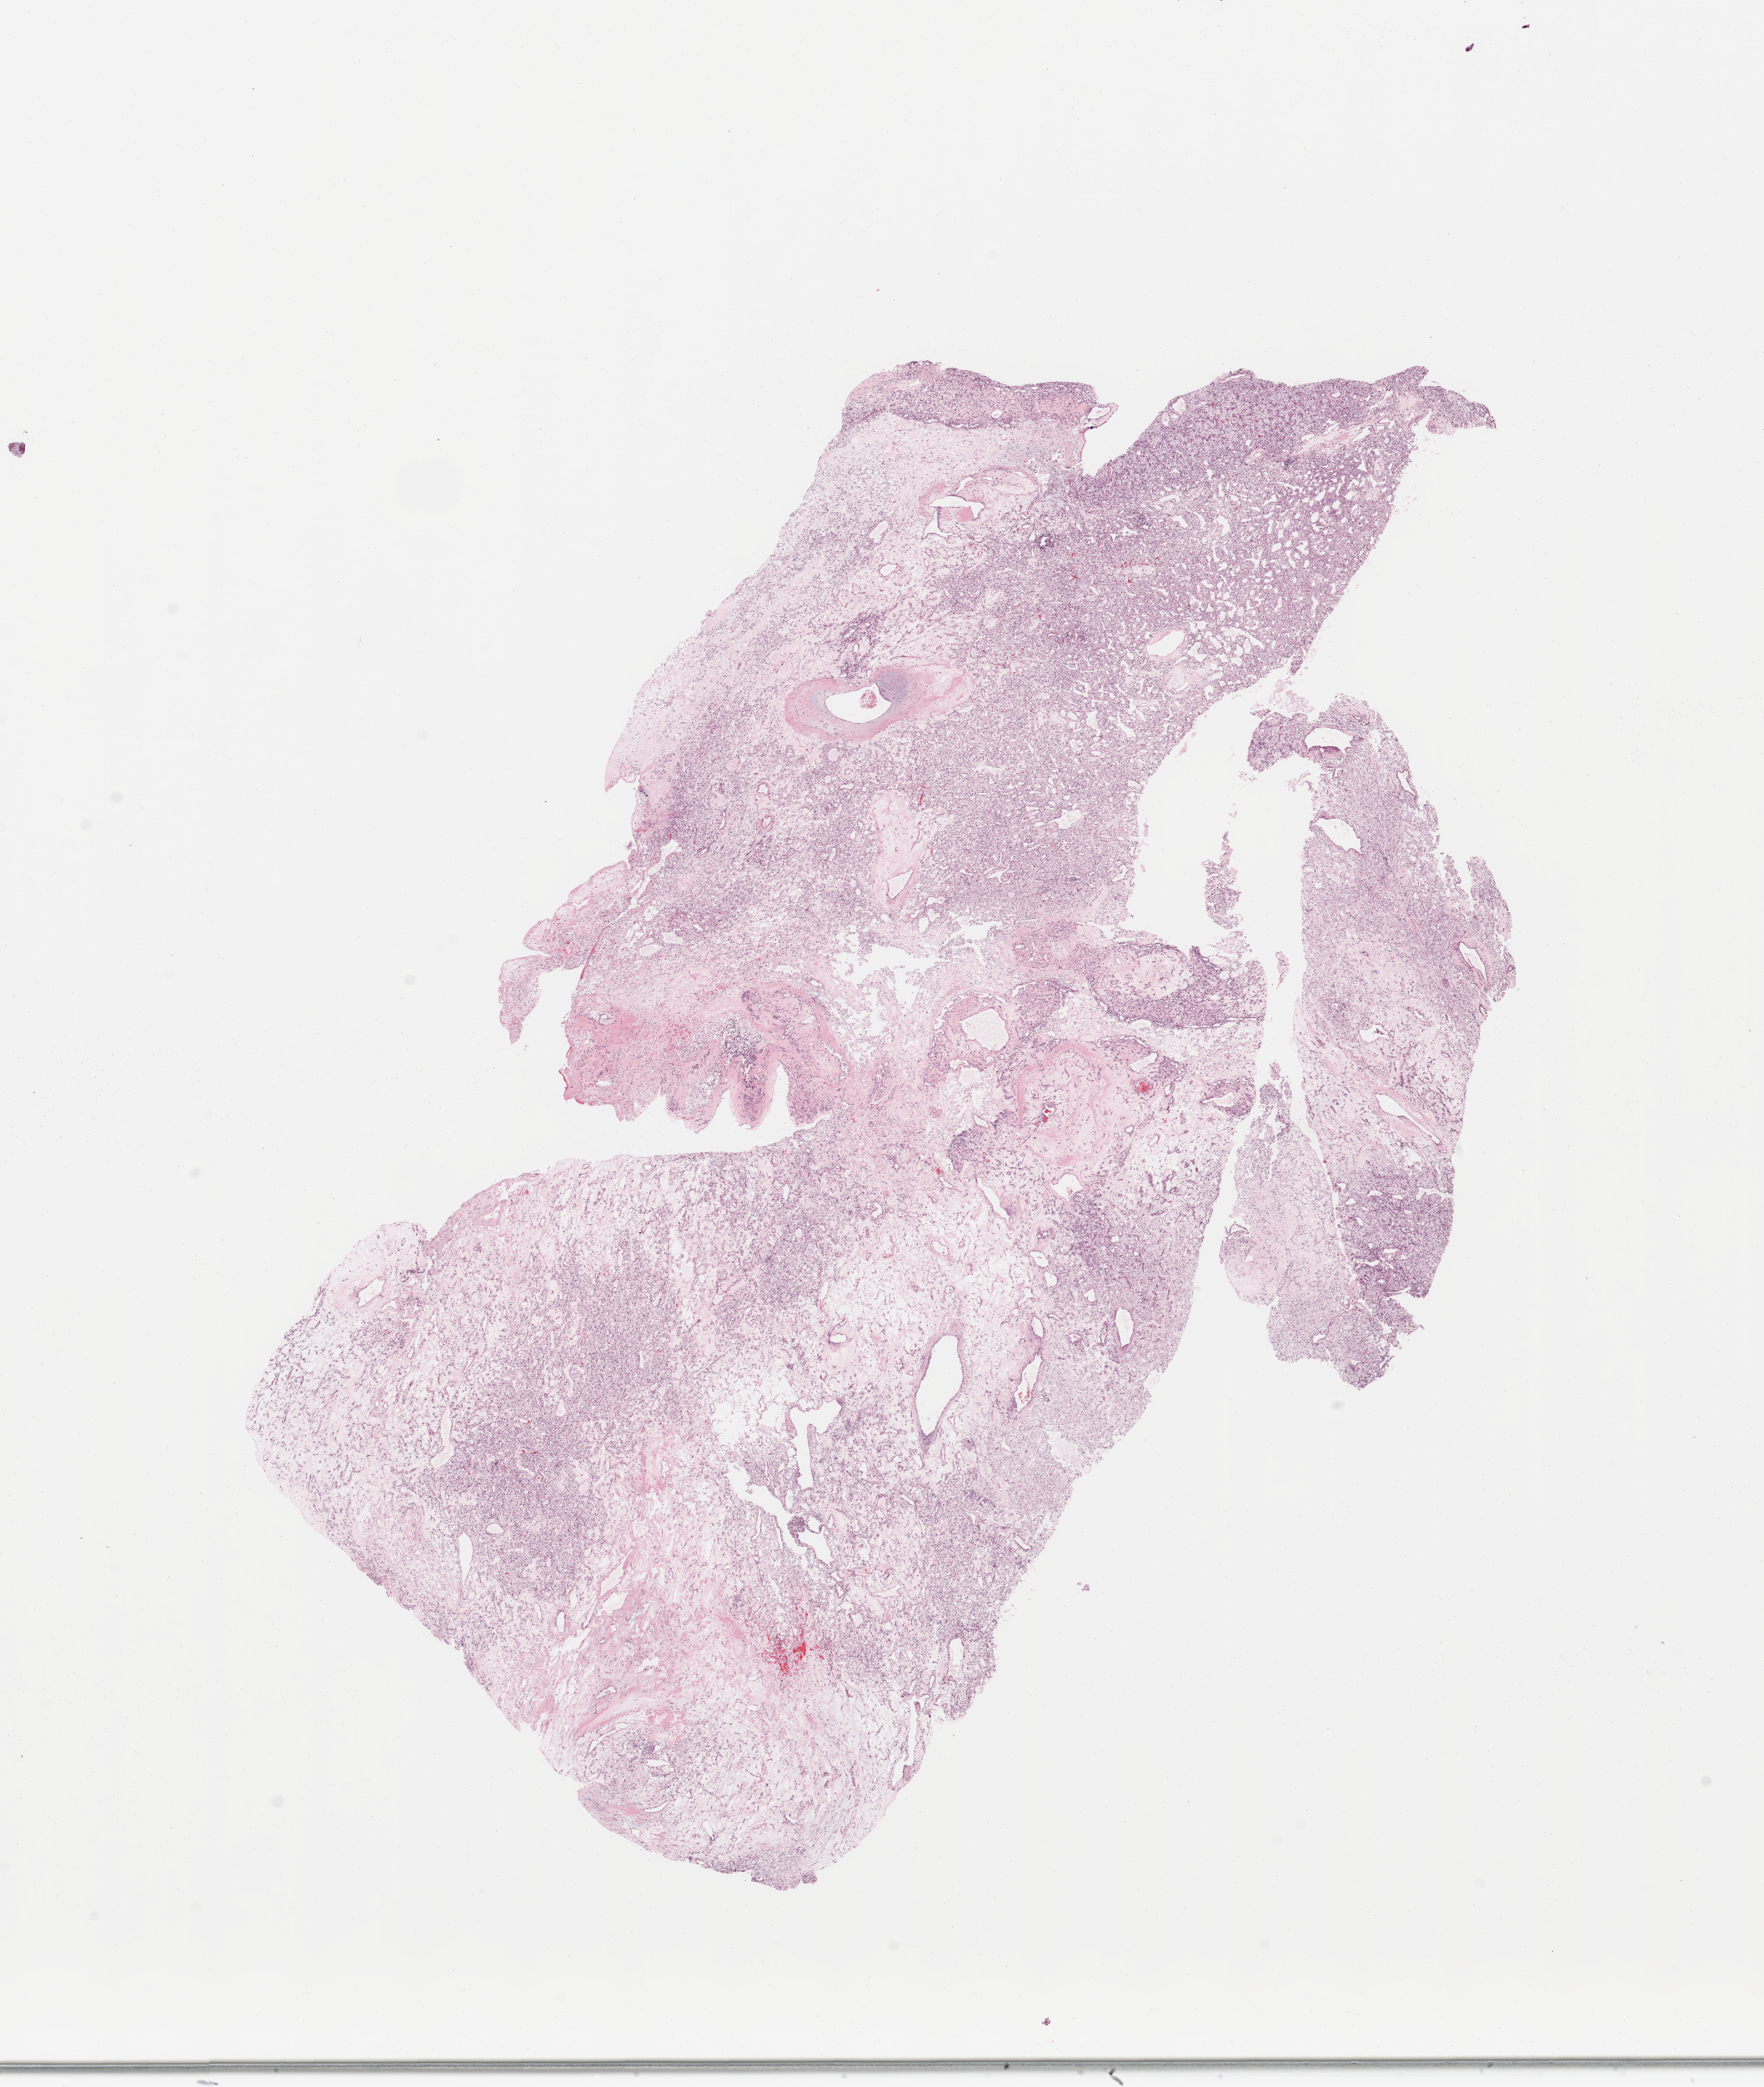
Whole-slide histology image, H&E, a low-resolution overview of the entire scanned area, about 16.7 x 19.8 mm. Tumour tissue sample, kidney. Patient: male, age 67 years. Histologic grade: G4 (undifferentiated).
Primary tumour site (as recorded): upper pole. Histologic diagnosis: Renal cell carcinoma, NOS. AJCC pathologic stage: III.